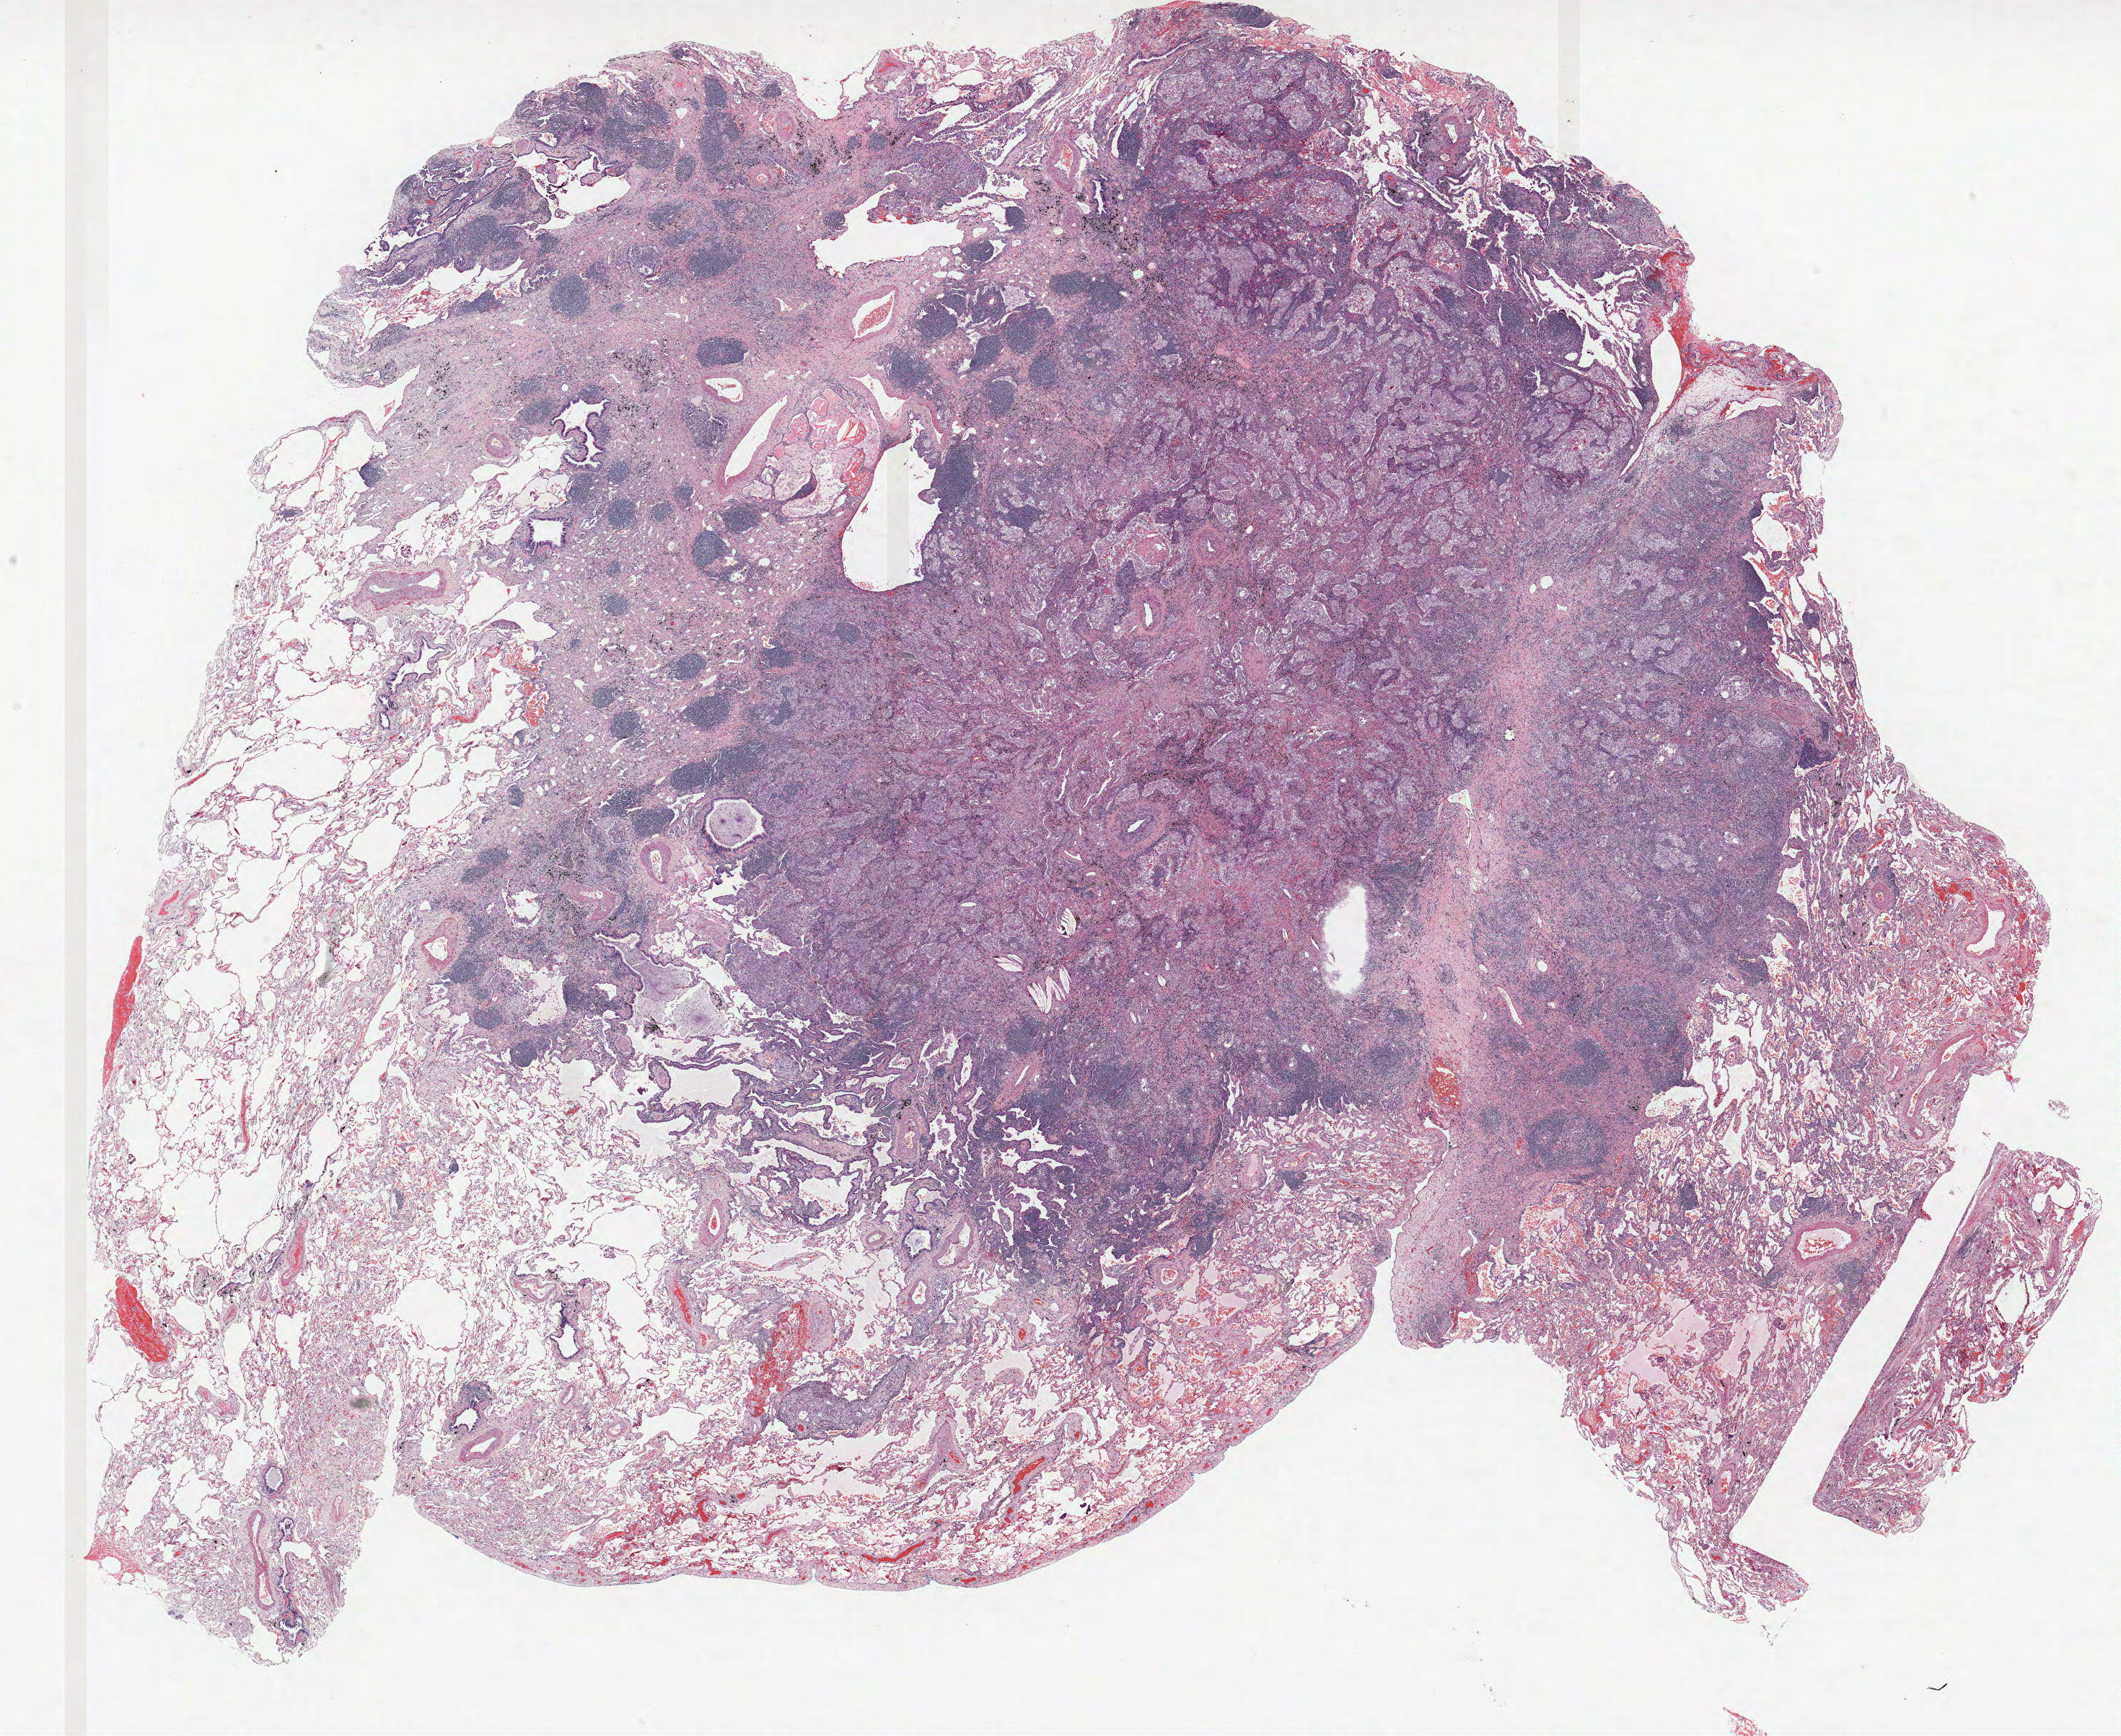
H&E-stained whole-slide image — a low-resolution overview of the entire scanned area, about 23.5 x 19.3 mm; FFPE section; lung tissue. Female patient, aged 61 at enrolment. Grade: poorly differentiated (G3).
Stage (AJCC 6th edition): IIIA. Primary tumour location (clinical record): right upper lobe. Participant's lung-cancer diagnosis: Adenocarcinoma, NOS. Tumour size (pathology): 22 mm.